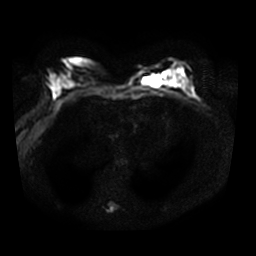
Breast MRI, one axial slice; slice 19 of 34 in the series (ordered by position); diffusion-weighted series; image 2 of 4 stored at this slice position (different b-values; order by instance number); 3 T; 5 mm slice thickness; 256 × 256 image matrix, field of view 340 × 340 mm. Female patient.
Annotated regions visible in this slice (outlined manually by an expert reader):
- tumour on diffusion-weighted imaging: bounding box <147,75,165,88> (left, top, right, bottom; pixels)